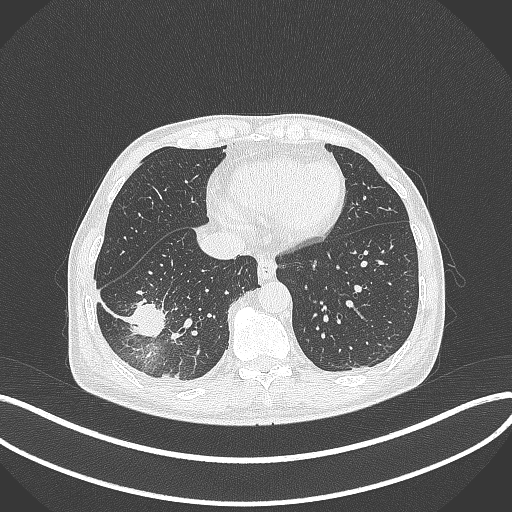
Chest CT, one axial slice; slice 105 of 388 in the series (ordered by position); lung window (W 1500 / L -600 HU); 512 × 512 image matrix, field of view 400 × 400 mm. Patient: male, 64 years. From the clinical record (not read from this slice): clinical TNM (as recorded): T3 N0 M0; histopathological grade: G2-3.
Structures marked on this image (rectangle marked by the reading radiologist):
- lung tumour (recorded histology: adenocarcinoma): bounding box <124,293,170,346> (left, top, right, bottom; pixels)